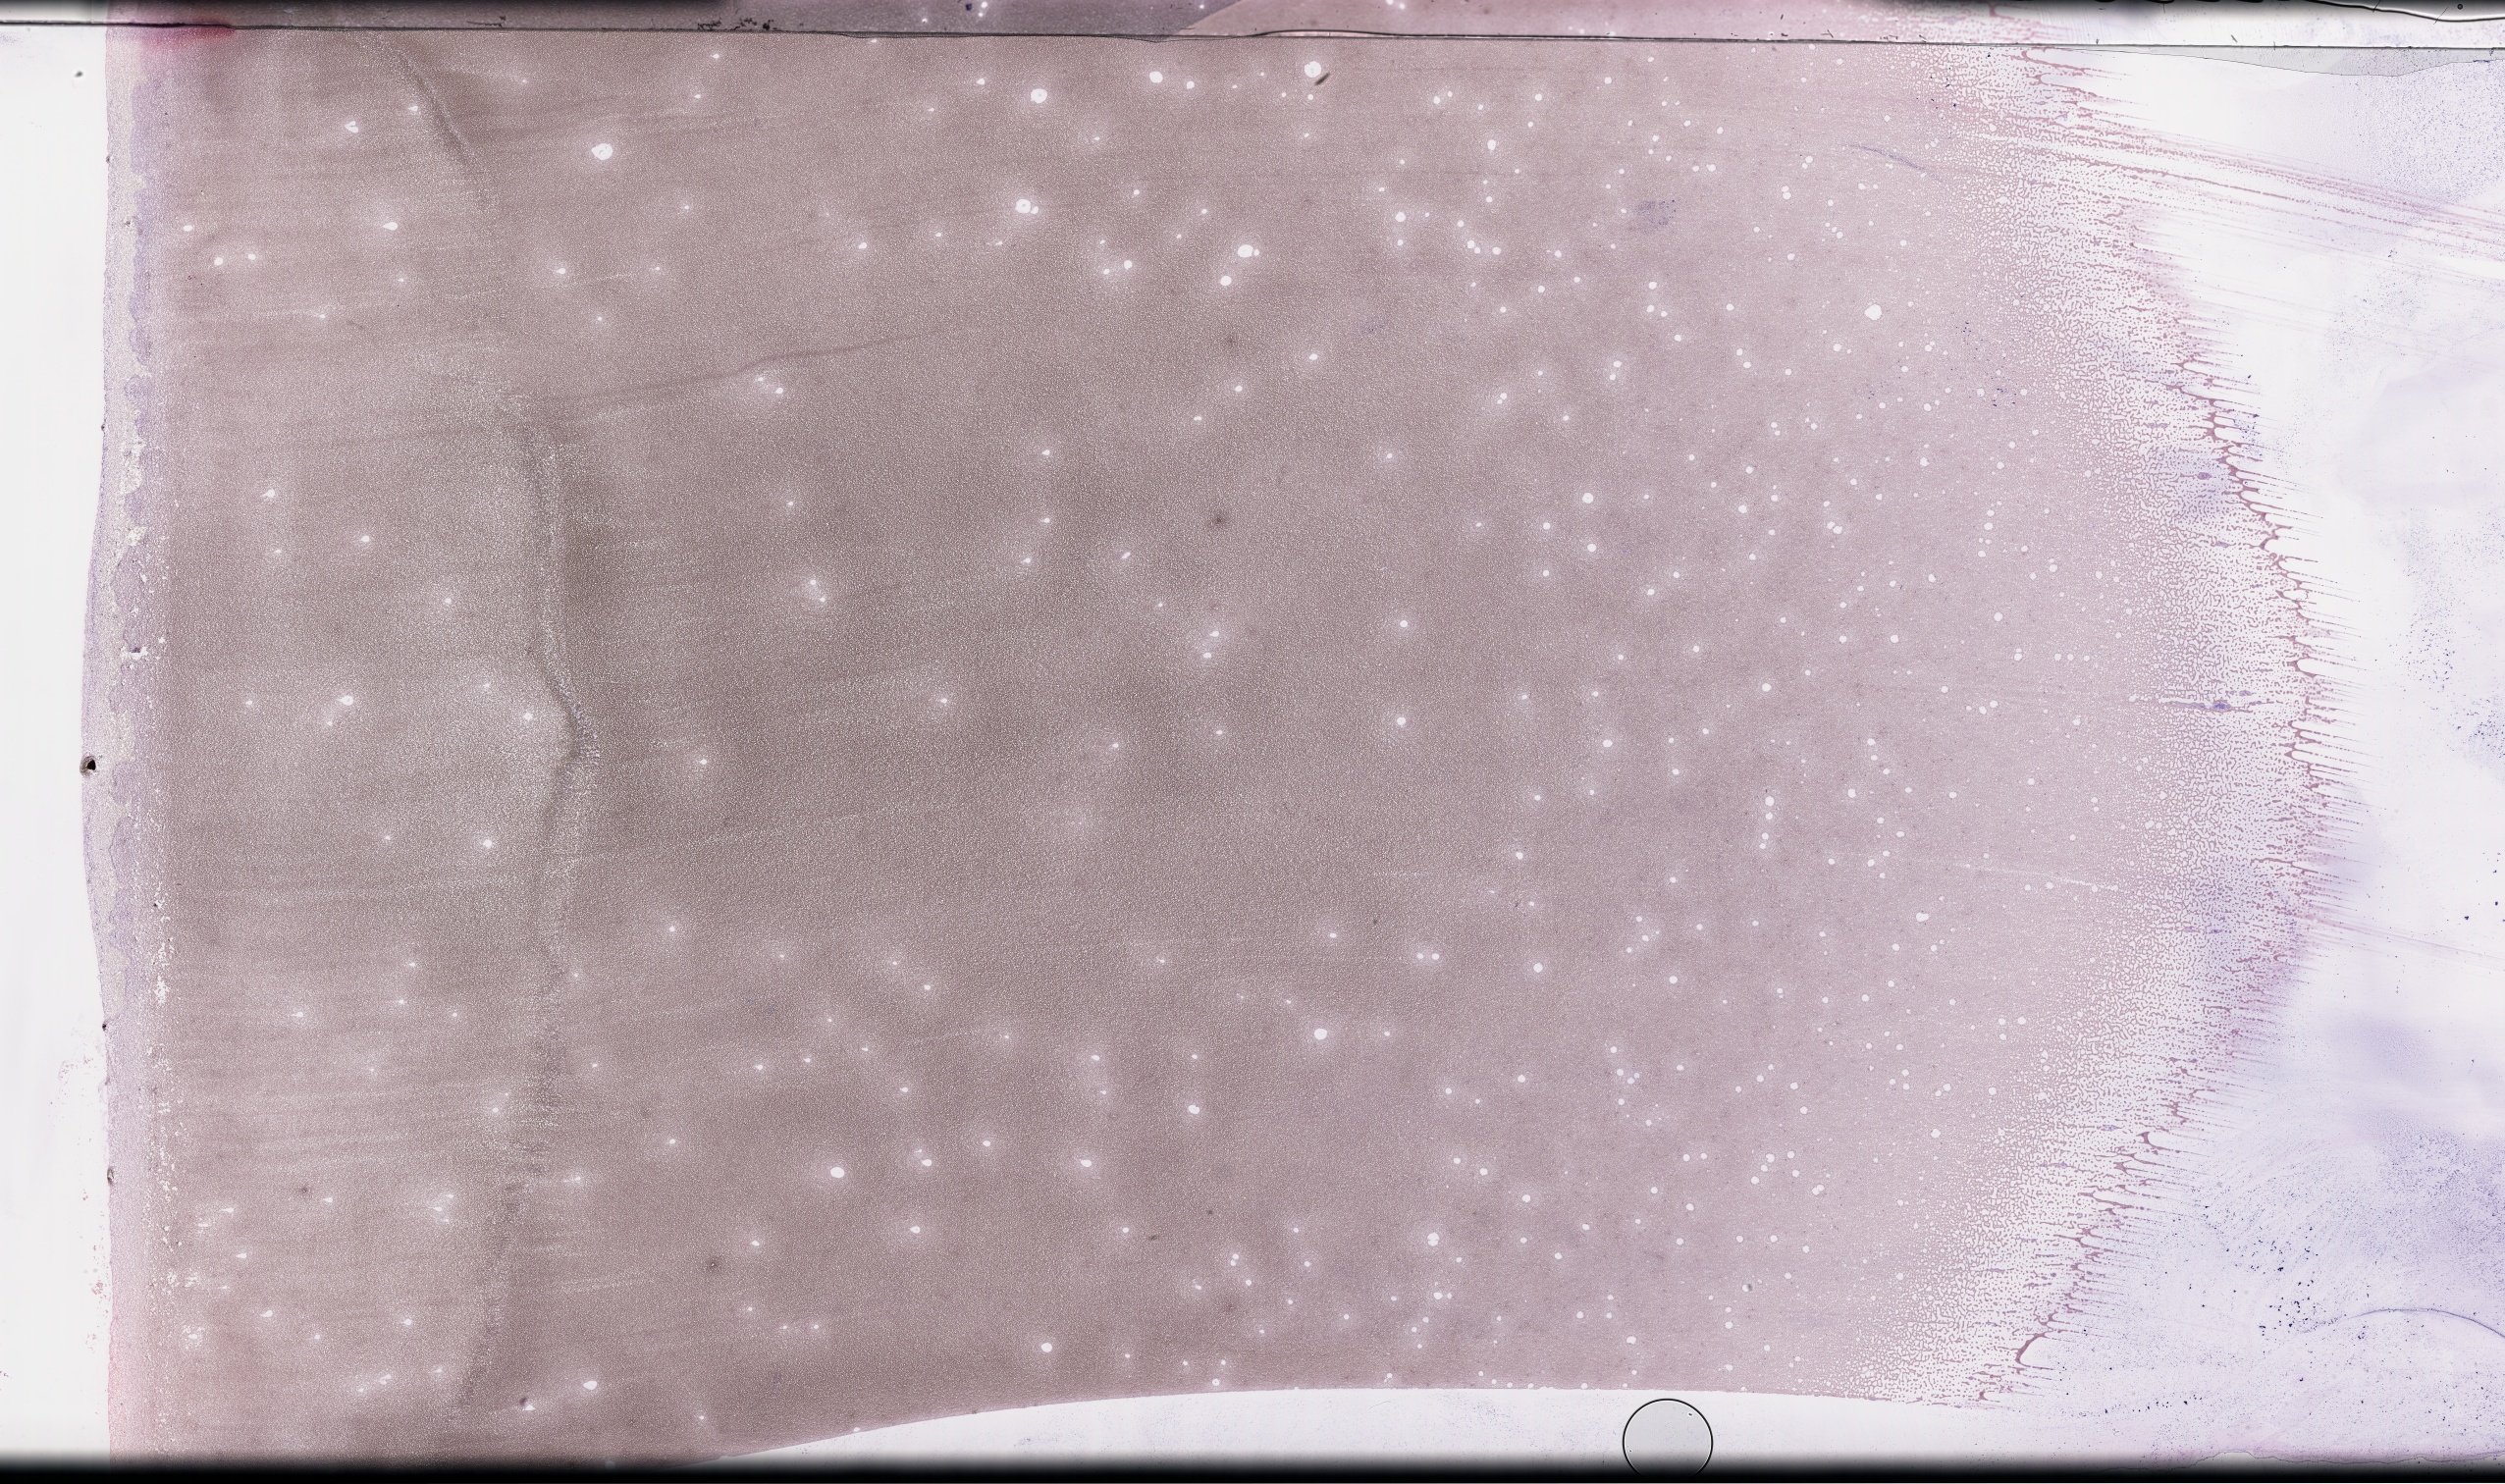
Wright-Giemsa-stained whole blood smear, whole-slide image — shown as a low-resolution overview of the whole scanned area (about 41.2 x 24.4 mm); EDTA-anticoagulated smear; collected on treatment. Male patient.
• from a patient with: Plasma Cell Myeloma